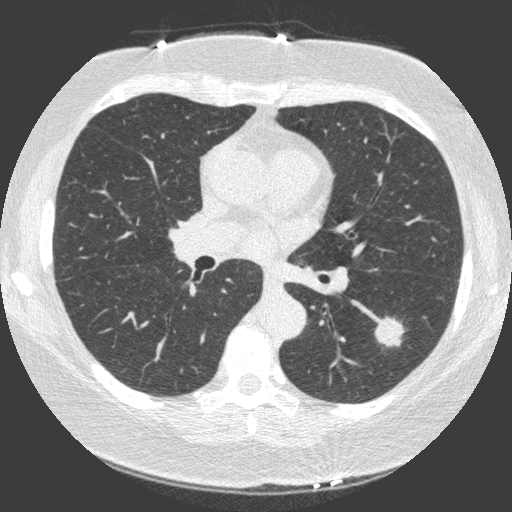
Chest CT (low-dose screening protocol), one axial image. Third annual screen. Lung window (W 1500 / L -600 HU). 1 mm slice thickness. Slice 62 of 149 in the series. 512 × 512 image matrix. Female, age 66 years at enrolment. Current smoker at enrolment.
- Lesion marked by an expert reader, box from (x=365, y=302) to (x=421, y=353) px.
- Screening reader's record for this exam (one nodule recorded; not confirmed to be the boxed lesion): non-calcified nodule or mass ≥4 mm, left lower lobe, 23 × 17 mm, spiculated (stellate) margins, soft tissue attenuation, pre-existing on the prior screen: yes; interval growth: yes.